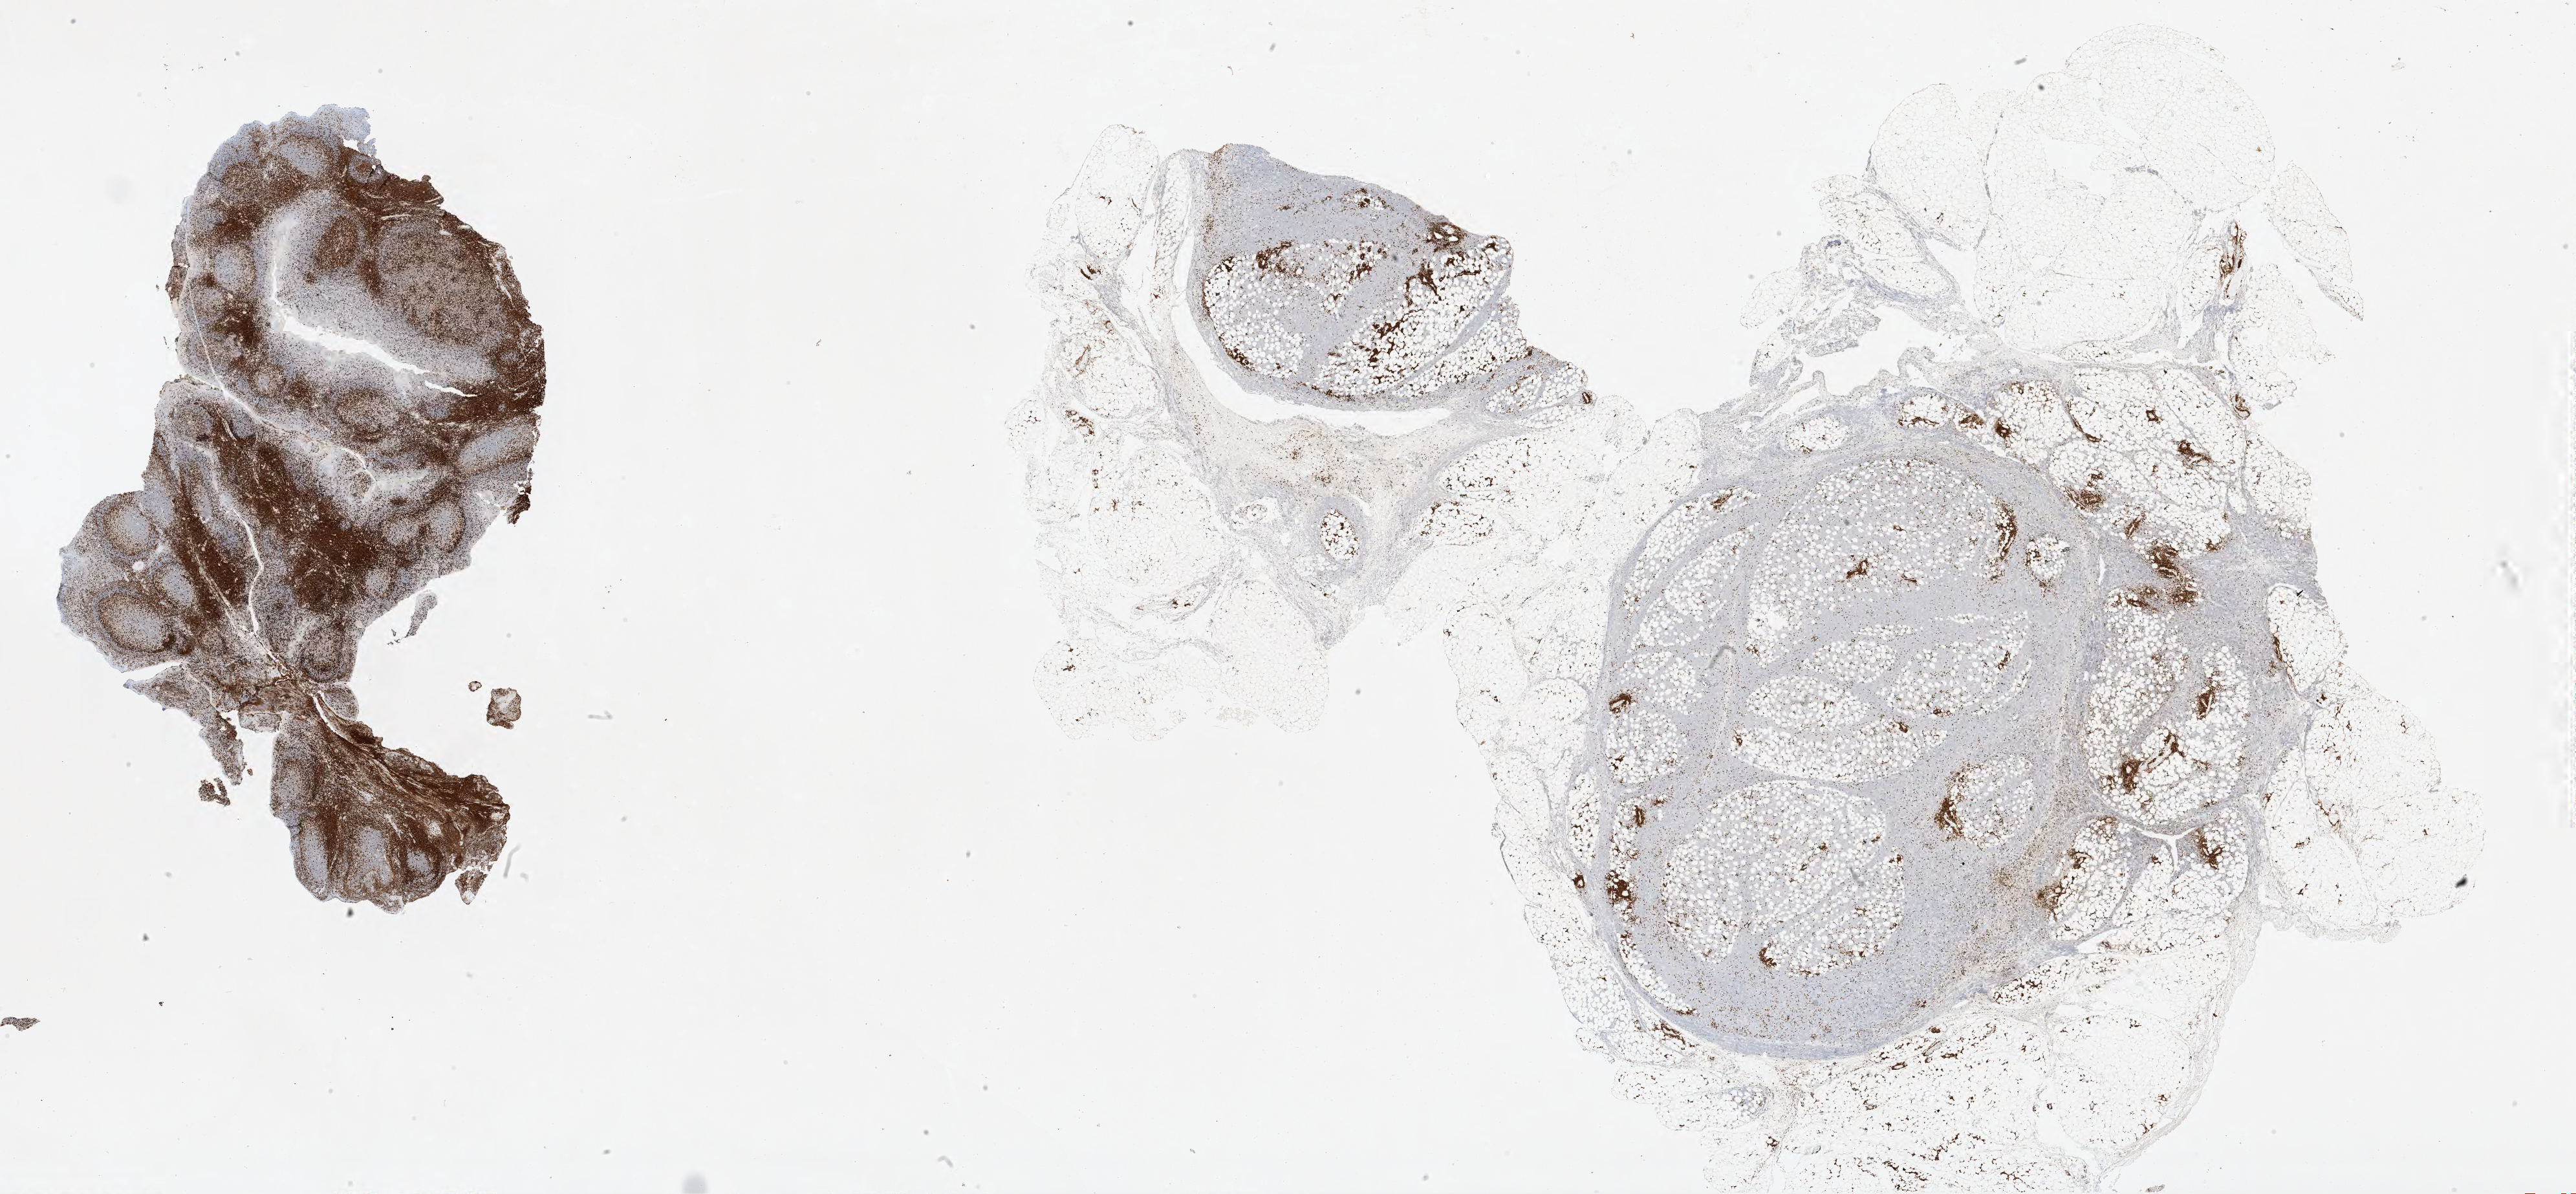
IHC for CD3, whole-slide image — low-resolution overview of the scanned area, about 32.0 x 14.8 mm. Tumor tissue. Patient: male, 24 years old.
* diagnosis: Burkitt lymphoma, NOS